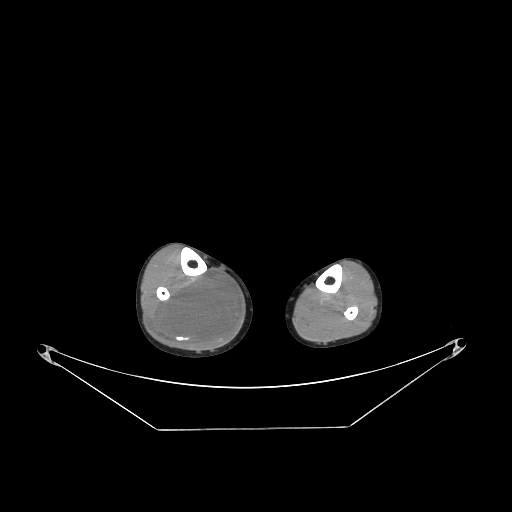
CT of an extremity soft-tissue mass (from a PET/CT study), one axial slice. Position 95 of 267 along the scan axis. 140 kVp. Soft-tissue window (W 400 / L 40 HU). 512 × 512 image matrix, field of view 500 × 500 mm. Male patient. From the clinical record (not read from this slice): histological type: liposarcoma - round cell; grade: high; site of the primary tumour: right calf.
Structures marked on this image (expert contour drawn on MRI and transferred to this co-registered scan by the dataset authors):
- gross tumour volume (mass): box from (x=151, y=271) to (x=241, y=350) px